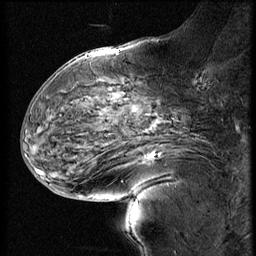
Breast MRI (dynamic contrast-enhanced), one sagittal slice. Position 26 of 60 along the scan axis. 4 images stored at this slice position (order not interpretable as contrast timing). 1.5 T. TE 4.2 ms, TR 9 ms. 2.5 mm slice thickness. 256 × 256 image matrix, field of view 180 × 180 mm. Patient: female, 56 years. Case-level facts recorded for this patient, not image findings: setting: breast cancer imaged before/during neoadjuvant chemotherapy; receptor status: HER2-positive.
Structures marked on this image (semi-automatically segmented with operator editing):
- analysis volume of interest (the breast-tissue region the enhancement analysis was run in; not a lesion): bounding box <110,138,192,201> (left, top, right, bottom; pixels)
- tumour enhancement mask (voxels above the 140 % enhancement threshold inside the analysis volume of interest): <146,155,154,161>